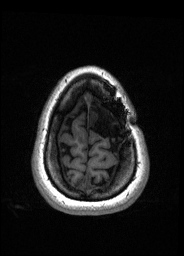
Pre-operative brain MRI before brain-tumour surgery, one axial slice; slice 34 of 176 in the series (ordered by position); T1-weighted post-contrast; 184 × 256 image matrix, field of view 180 × 250 mm. From the clinical record (not read from this slice): histopathology: Oligodendroglioma; WHO grade: 2; IDH mutation: yes; tumour location: Left Frontal.
Outlined on this slice (manually delineated by an expert):
- tumour: bounding box <88,111,99,127> (left, top, right, bottom; pixels)